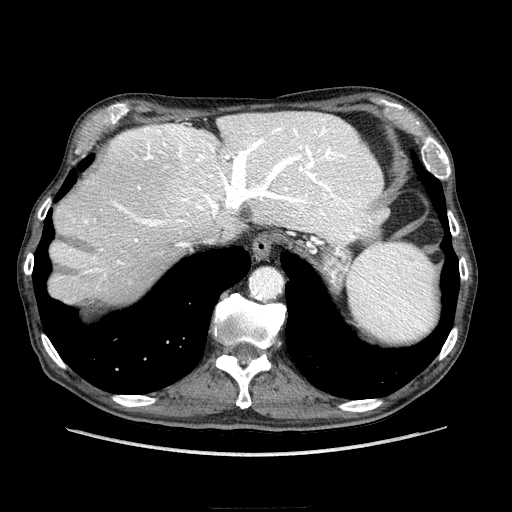
Contrast-enhanced abdominal CT (liver protocol), one axial slice; soft-tissue window (W 400 / L 40 HU); 512 × 512 image matrix. Case-level facts recorded for this patient, not image findings: diagnosis: hepatocellular carcinoma (patient treated with transarterial chemoembolisation; whether this scan precedes or follows treatment is not stated here); TNM stage (as recorded): Stage-IIIA; Child-Pugh class: A; tumour differentiation: well differentiated; tumour nodularity: multinodular.
Outlined on this slice (semi-automatically segmented with operator editing):
- abdominal aorta: box from (x=250, y=269) to (x=280, y=297) px
- liver parenchyma outside the tumour (the mass and vessels are separate outlines, so this box may not span the whole liver): (x=50, y=112)–(x=384, y=304)
- liver vessels: (x=53, y=116)–(x=380, y=276)